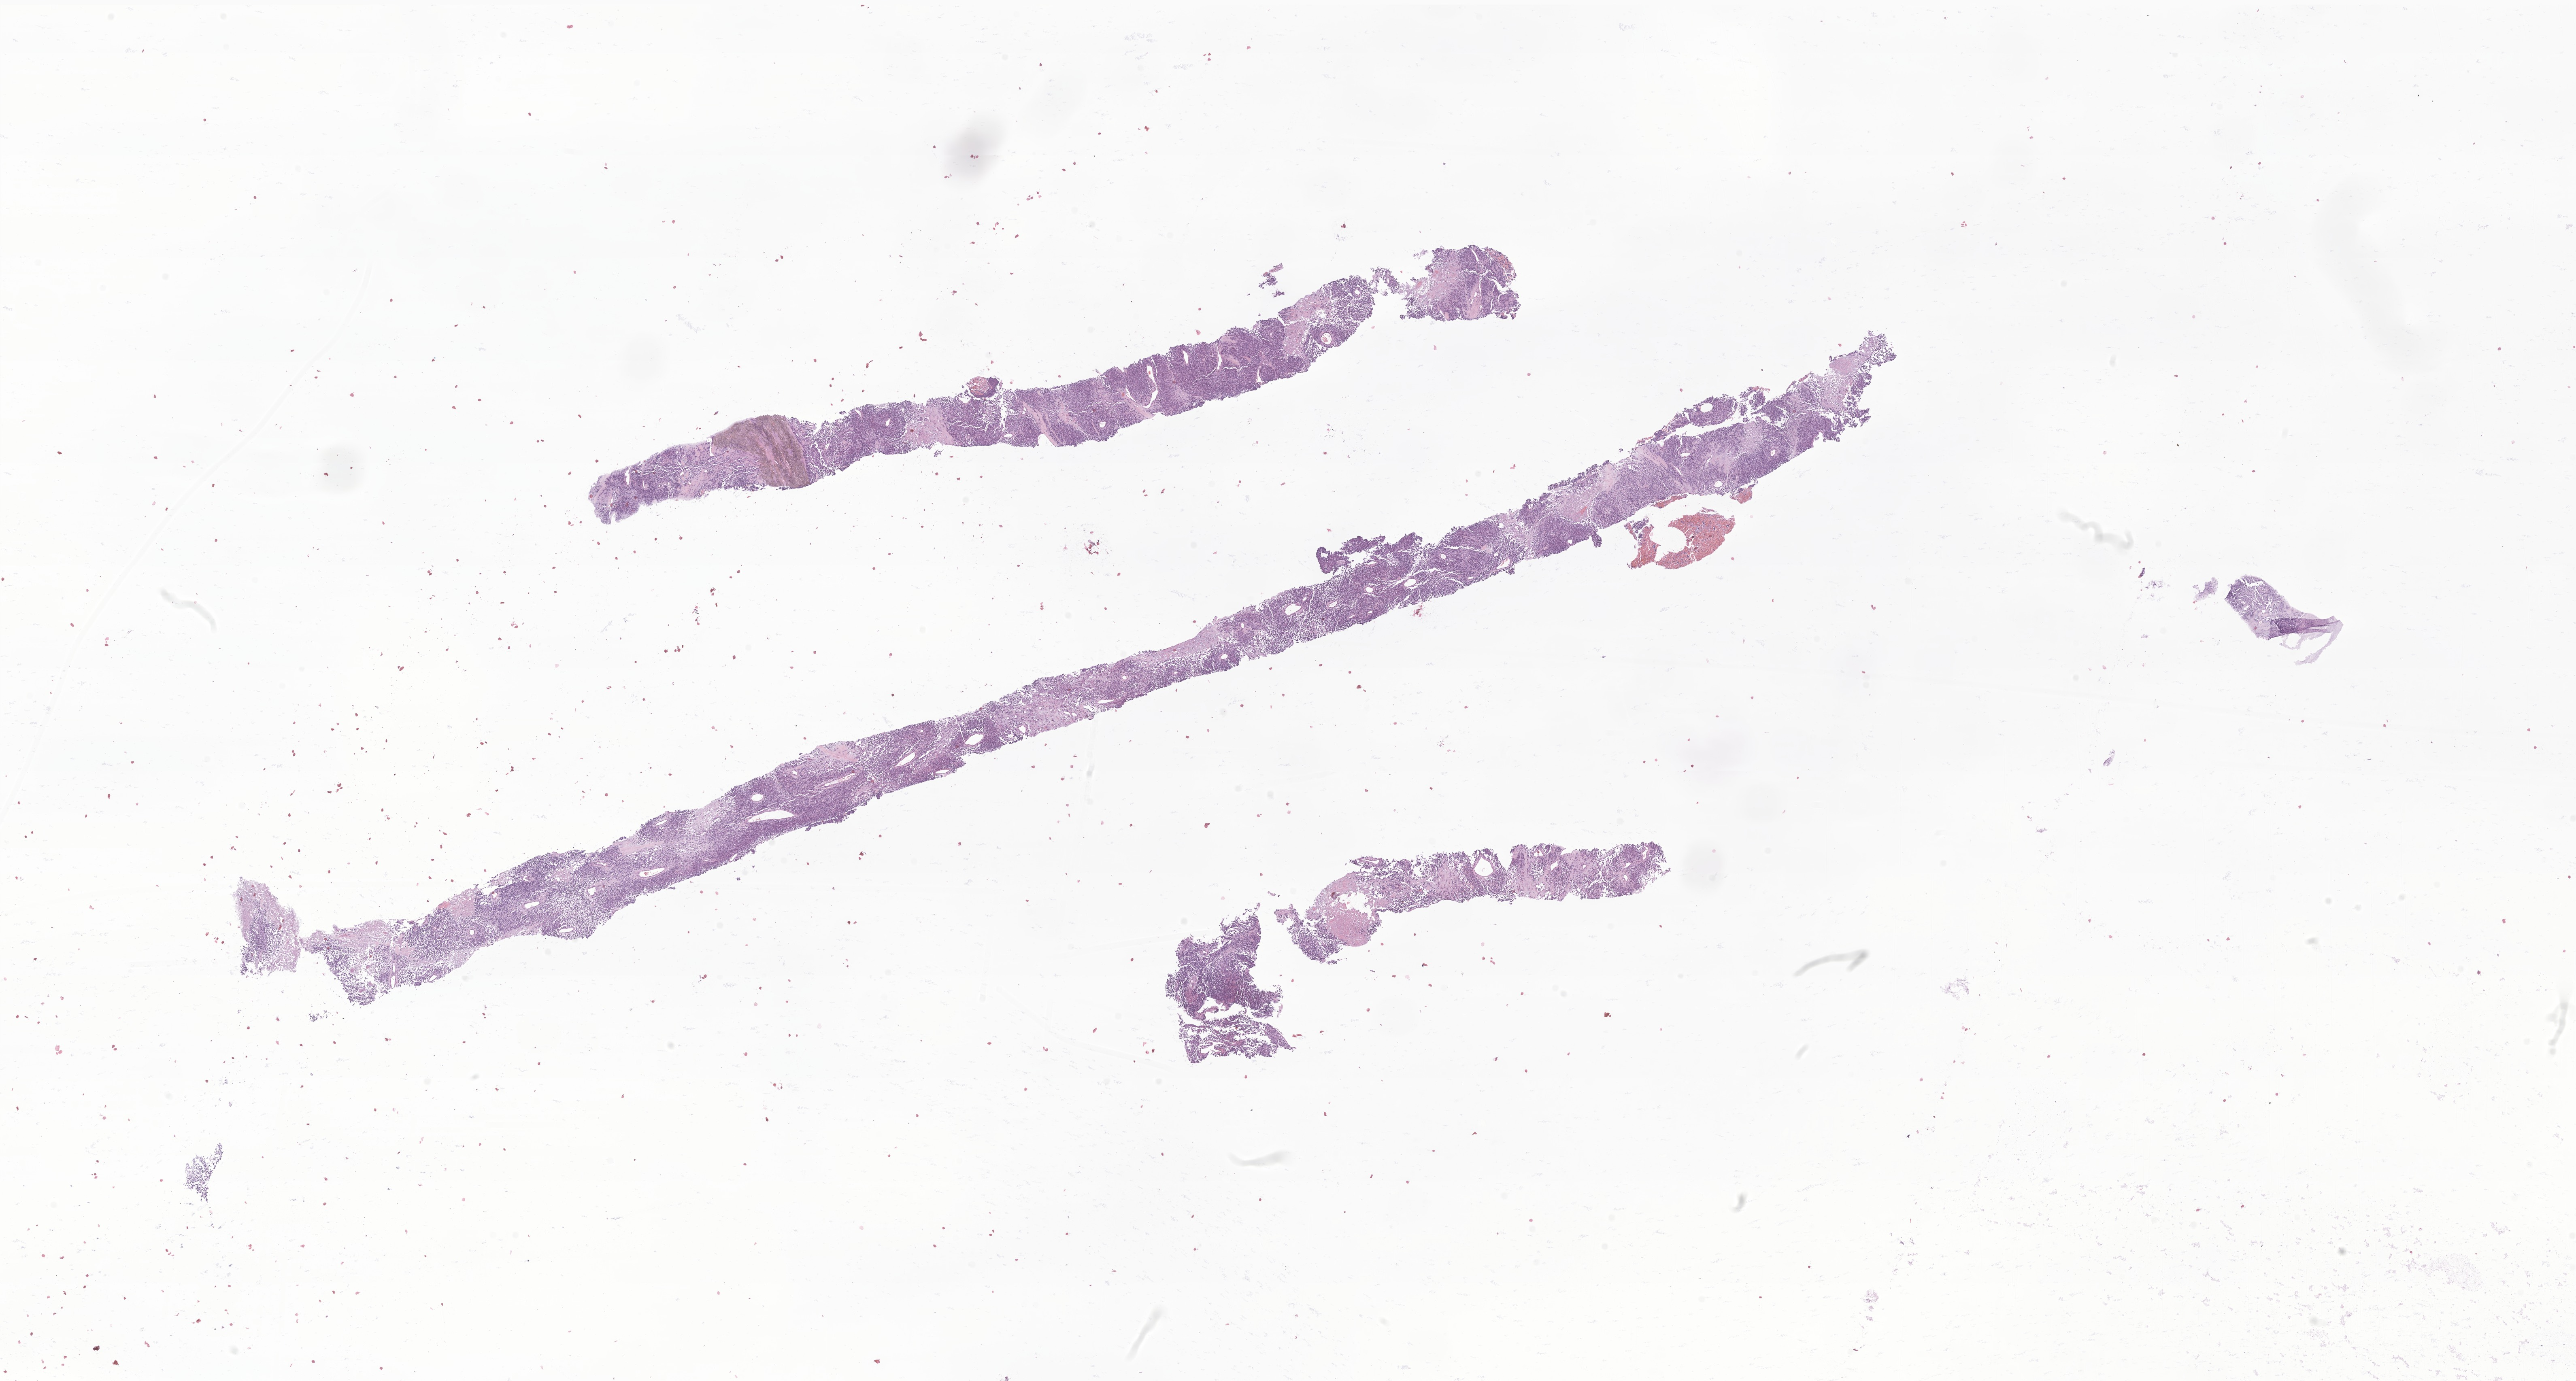
Hematoxylin and eosin (H&E) whole-slide image of tumor tissue from the soft tissue of upper extremity — whole scanned area (about 26.8 x 14.4 mm) shown as a low-resolution overview. Formalin-fixed, paraffin-embedded (FFPE) tissue. Patient male; age 127 months (10 years 7 months).
Recorded diagnosis: Alveolar rhabdomyosarcoma.